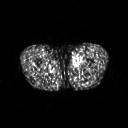
FDG PET of an extremity soft-tissue mass (from a PET/CT study), one axial slice. Slice 254 of 311 in the series (ordered by position). 3.27 mm slice thickness. 128 × 128 image matrix. Male patient, age 29 years. From the clinical record (not read from this slice): histological type: mixoid liposarcoma; grade: low; site of the primary tumour: left thigh.
Outlined on this slice (expert contour drawn on MRI and transferred to this co-registered scan by the dataset authors):
- gross tumour volume (mass): bounding box [x1, y1, x2, y2] px = [71, 54, 82, 66]